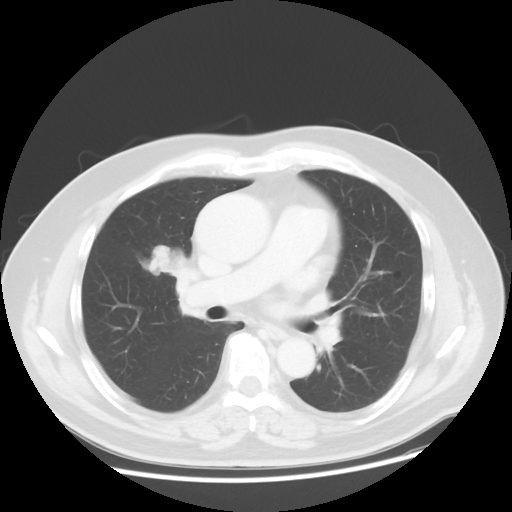
Chest CT, one axial slice. 120 kVp. Lung window (W 1500 / L -600 HU). 5 mm slice thickness. 512 × 512 image matrix, field of view 392 × 392 mm. Patient: male, 60 years. Case-level facts recorded for this patient, not image findings: clinical TNM (as recorded): T2 N3 M0.
Structures marked on this image (rectangle marked by the reading radiologist):
- lung tumour (recorded histology: adenocarcinoma): bounding box <122,225,186,291> (left, top, right, bottom; pixels)